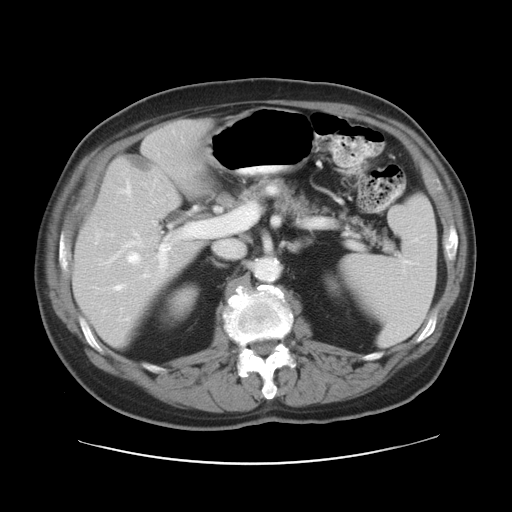
Contrast-enhanced abdominal CT, one axial slice; slice 16 of 28 in the series (ordered by position); reconstruction kernel STANDARD; 120 kVp; intravenous contrast given; soft-tissue window (W 400 / L 40 HU); 512 × 512 image matrix. Male patient, age 74 years. From the clinical record (not read from this slice): diagnosis: colorectal cancer liver metastases, imaged before liver resection; multiple liver metastases: no; largest metastasis: 5 cm; disease in both lobes: no.
Annotated regions visible in this slice (outlined manually by an expert reader):
- hepatic veins: box from (x=106, y=182) to (x=168, y=291) px
- liver: (x=74, y=123)–(x=207, y=345)
- planned liver remnant (the part of the liver to remain after resection): (x=74, y=173)–(x=193, y=345)
- portal vein (with intrahepatic branches): (x=159, y=223)–(x=199, y=268)
- liver metastasis: (x=131, y=157)–(x=152, y=171)